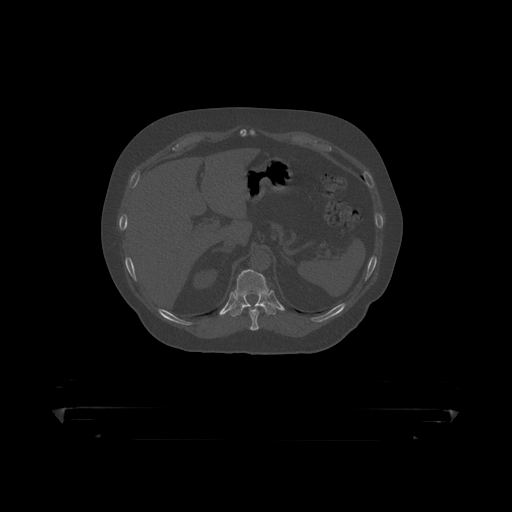
CT including the spine, one axial slice. Slice 201 of 390 in the series (ordered by position). Bone window (W 1800 / L 400 HU). 1.25 mm slice thickness. 512 × 512 image matrix, field of view 650 × 650 mm. Patient: male, 60 years. Case-level facts recorded for this patient, not image findings: primary cancer: prostate.
Outlined on this slice (semi-automatic segmentation, software-assisted and operator-edited):
- T10 vertebra: bounding box <249,305,261,319> (left, top, right, bottom; pixels)
- T11 vertebra: <225,270,280,316>